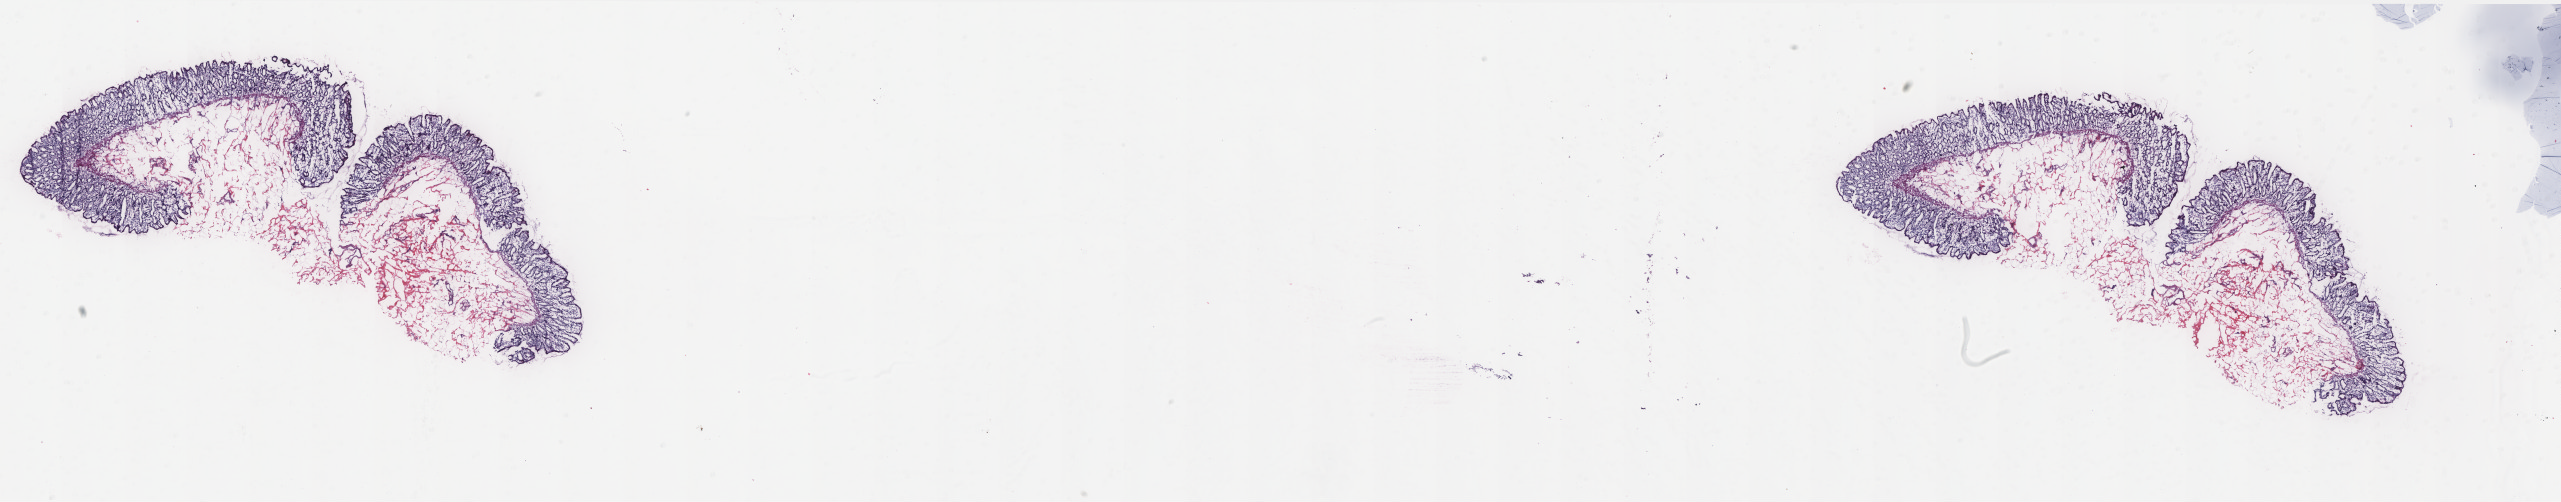
Digitized H&E tissue section (whole slide) — shown as a low-resolution overview of the whole scanned area (about 40.9 x 8.0 mm). Frozen section. Sample: solid tissue normal (non-tumour tissue), colon. Patient: male, age at initial diagnosis 82 years. Composition of this section per pathologist review: tumour cells 0%, normal cells 100%. Infiltration values recorded for this section: lymphocyte infiltration 35%, monocyte infiltration 10%, neutrophil infiltration 0%.
This section: solid tissue normal (non-tumour) sample from the same patient. Patient diagnosis: Adenocarcinoma, NOS (transverse colon).